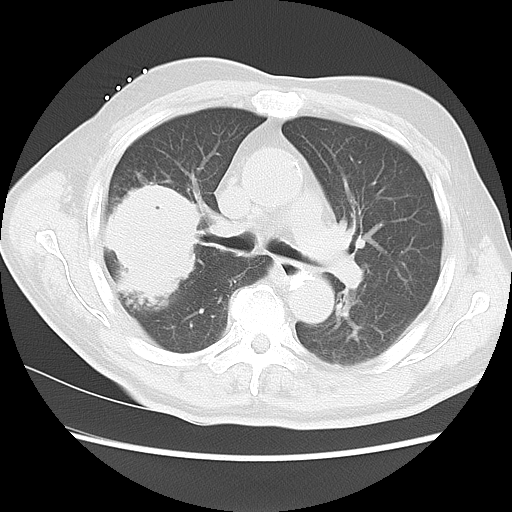
Chest CT, one axial slice. Position 8 of 15 along the scan axis. Reconstruction kernel LUNG. 120 kVp. Lung window (W 1500 / L -600 HU). 5 mm slice thickness. 512 × 512 image matrix. Patient: male, 68 years. From the clinical record (not read from this slice): clinical TNM (as recorded): T4 N3 M0.
Outlined on this slice (bounding box drawn by a radiologist):
- lung tumour (recorded histology: squamous cell carcinoma): bounding box <110,180,210,315> (left, top, right, bottom; pixels)